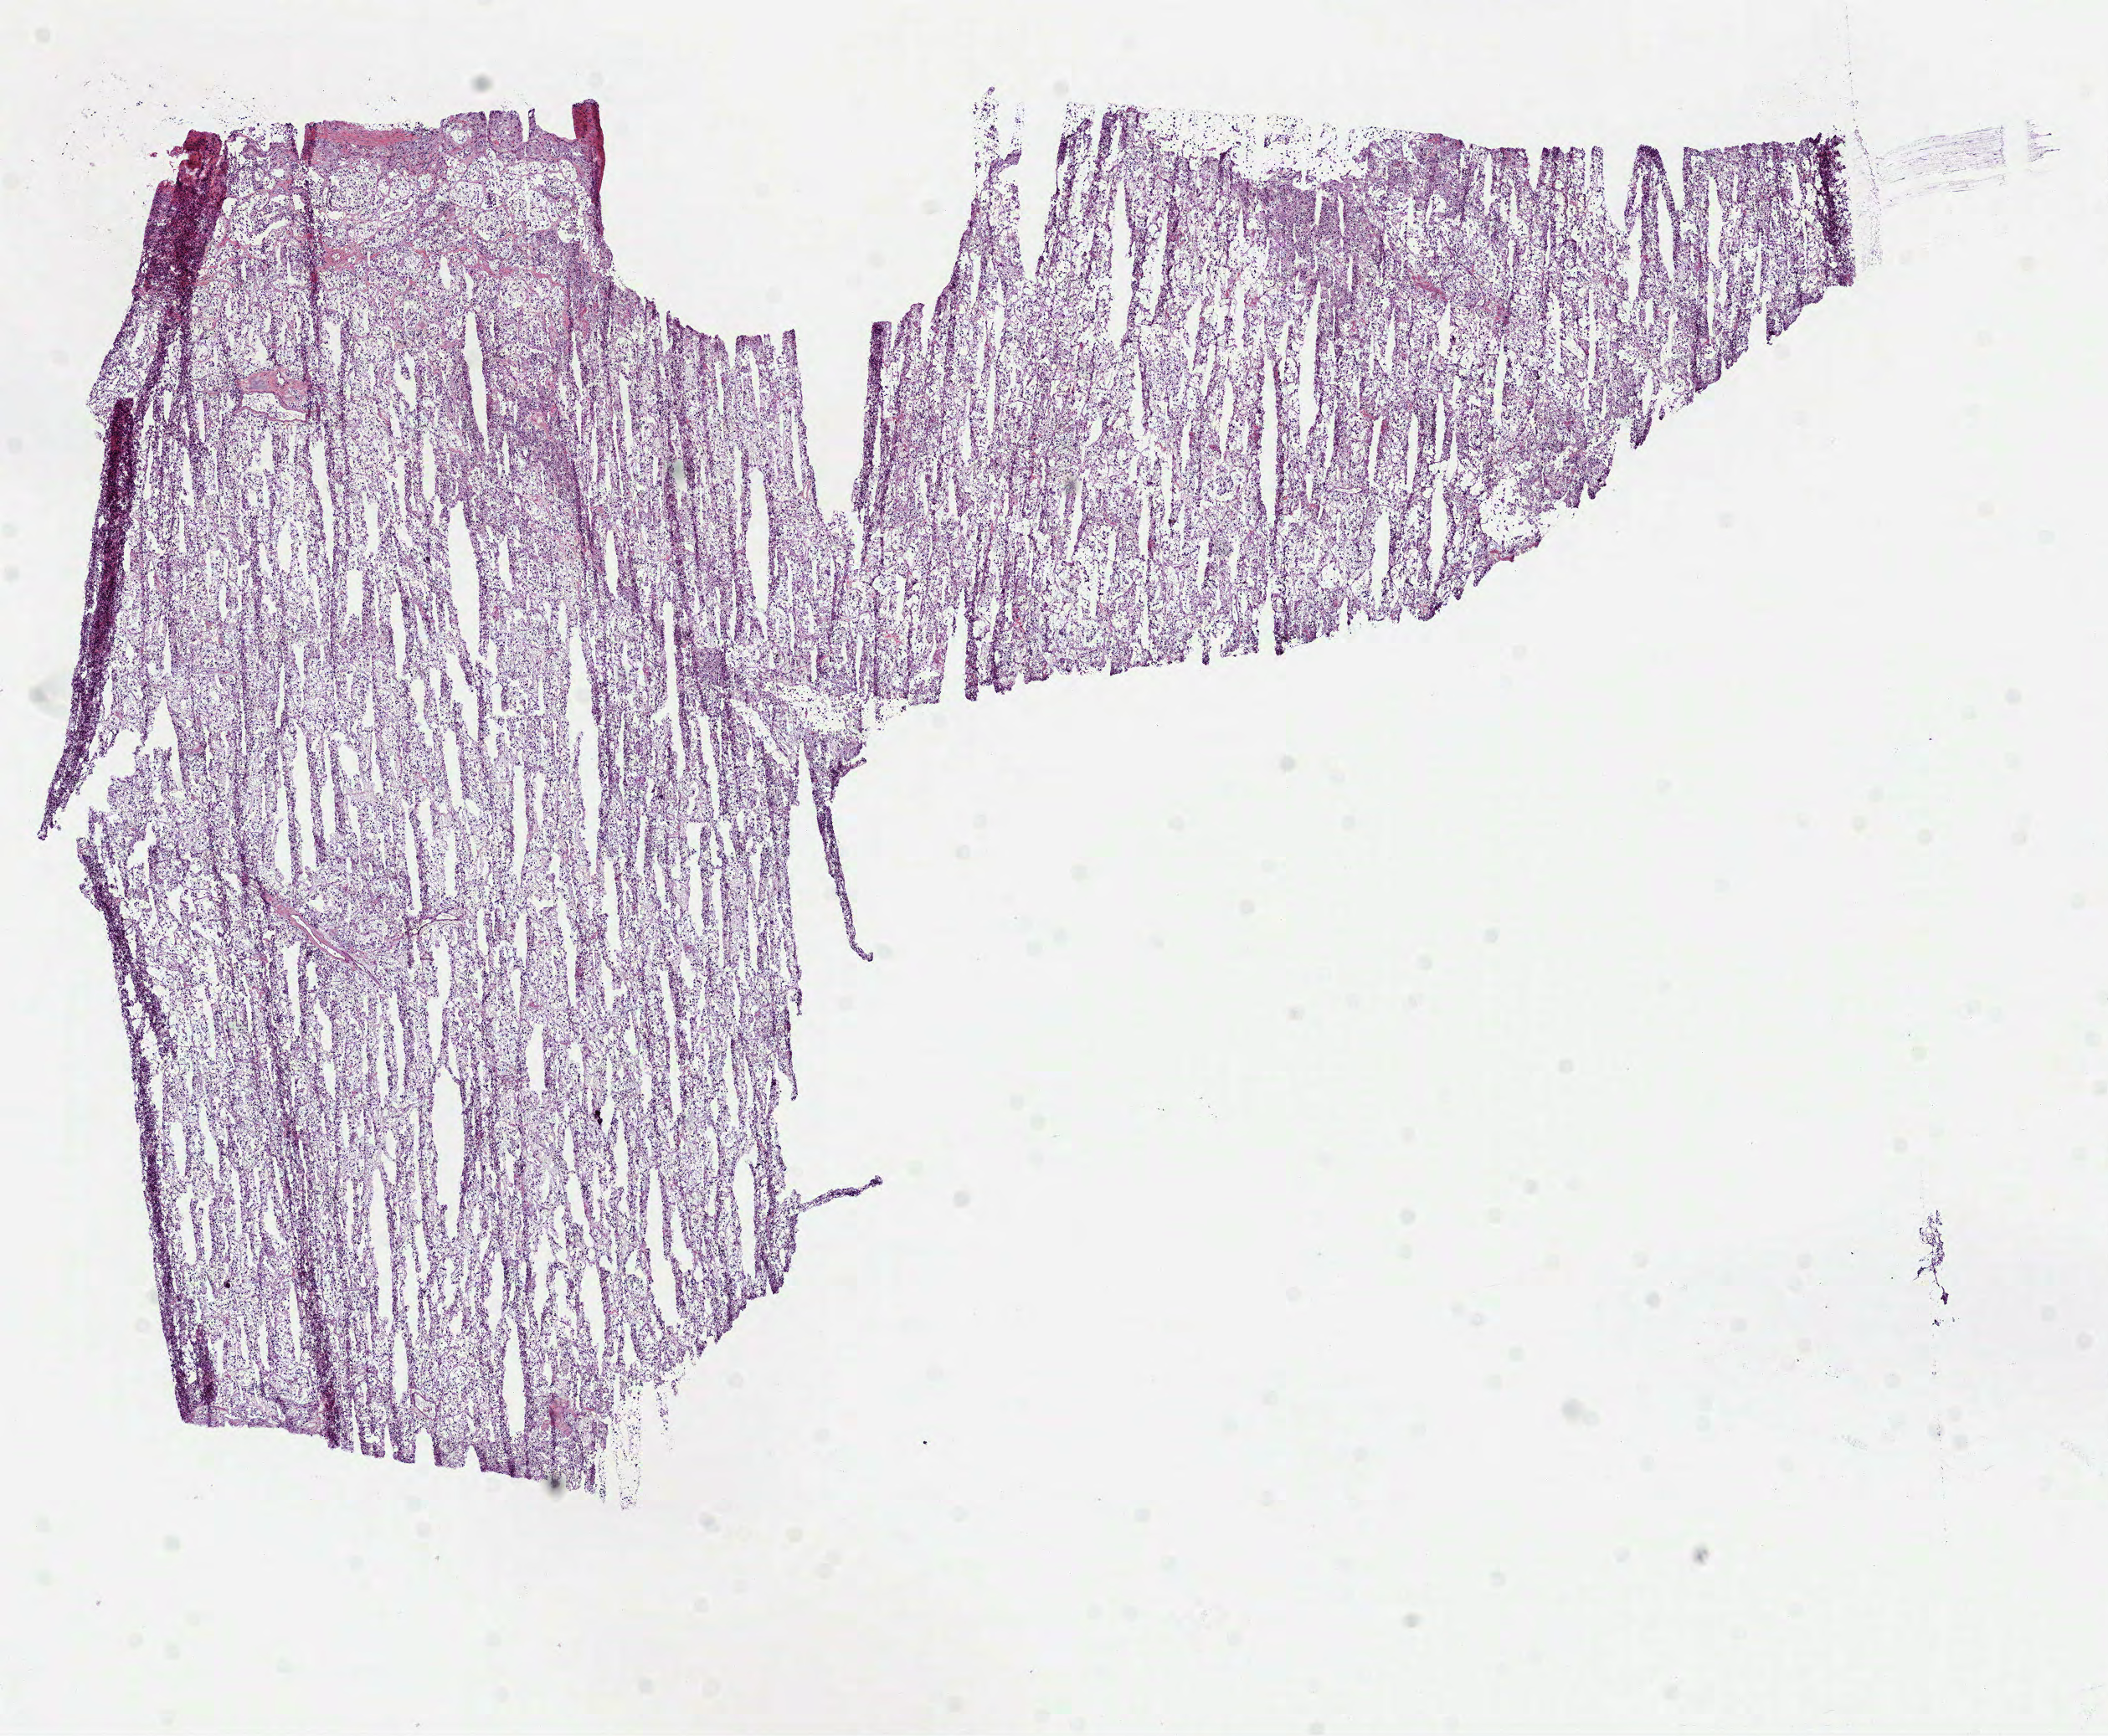
Digitized H&E tissue section (whole slide) — shown as a low-resolution overview of the whole scanned area (about 10.2 x 8.4 mm, slide scanned at 40x), frozen section from the bottom of the tissue portion, primary tumour sample from the kidney. Patient: female, age at initial diagnosis 38 years. Histologic grade: G2 (moderately differentiated). Pathologist review of this section (percent, as recorded): tumour cells 95%, tumour nuclei 90%, normal cells 0%, stromal cells 5%, necrosis 0%.
AJCC pathologic stage: I. Pathologic diagnosis: Clear cell adenocarcinoma, NOS.